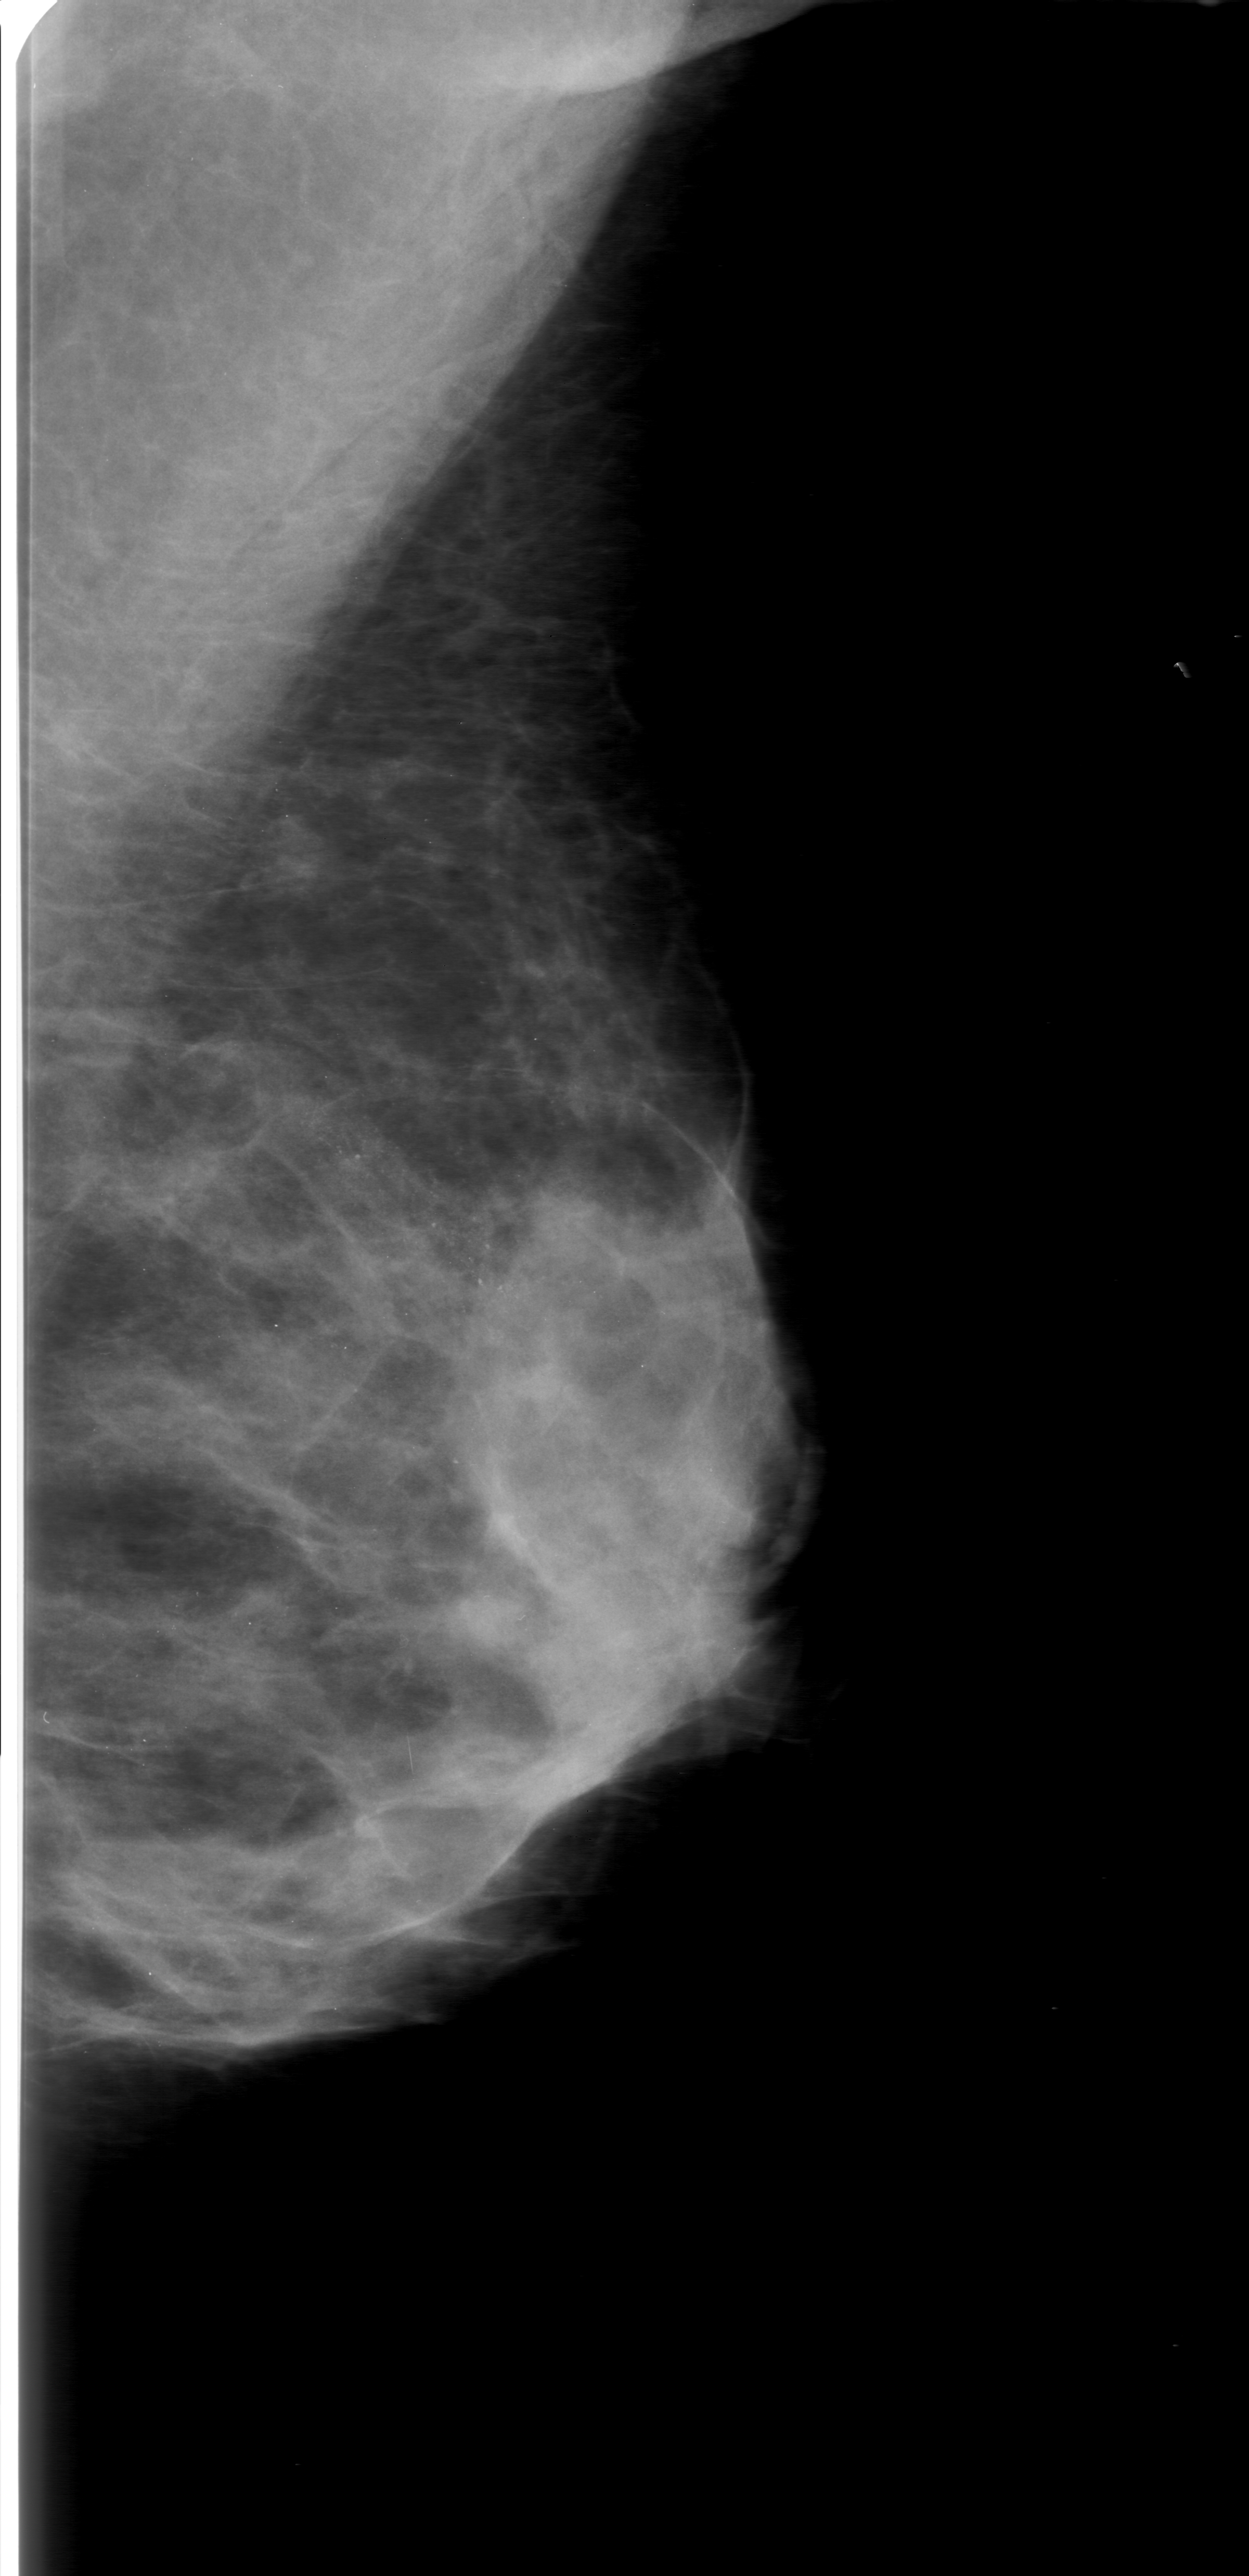
Mammogram (digitized film); left breast; MLO view.
- Marked findings (only marked abnormalities are described; nothing is implied about the rest of the image): calcifications, morphology amorphous, distribution segmental; BI-RADS assessment category 0 (incomplete: needs additional imaging); pathology (as recorded): benign.